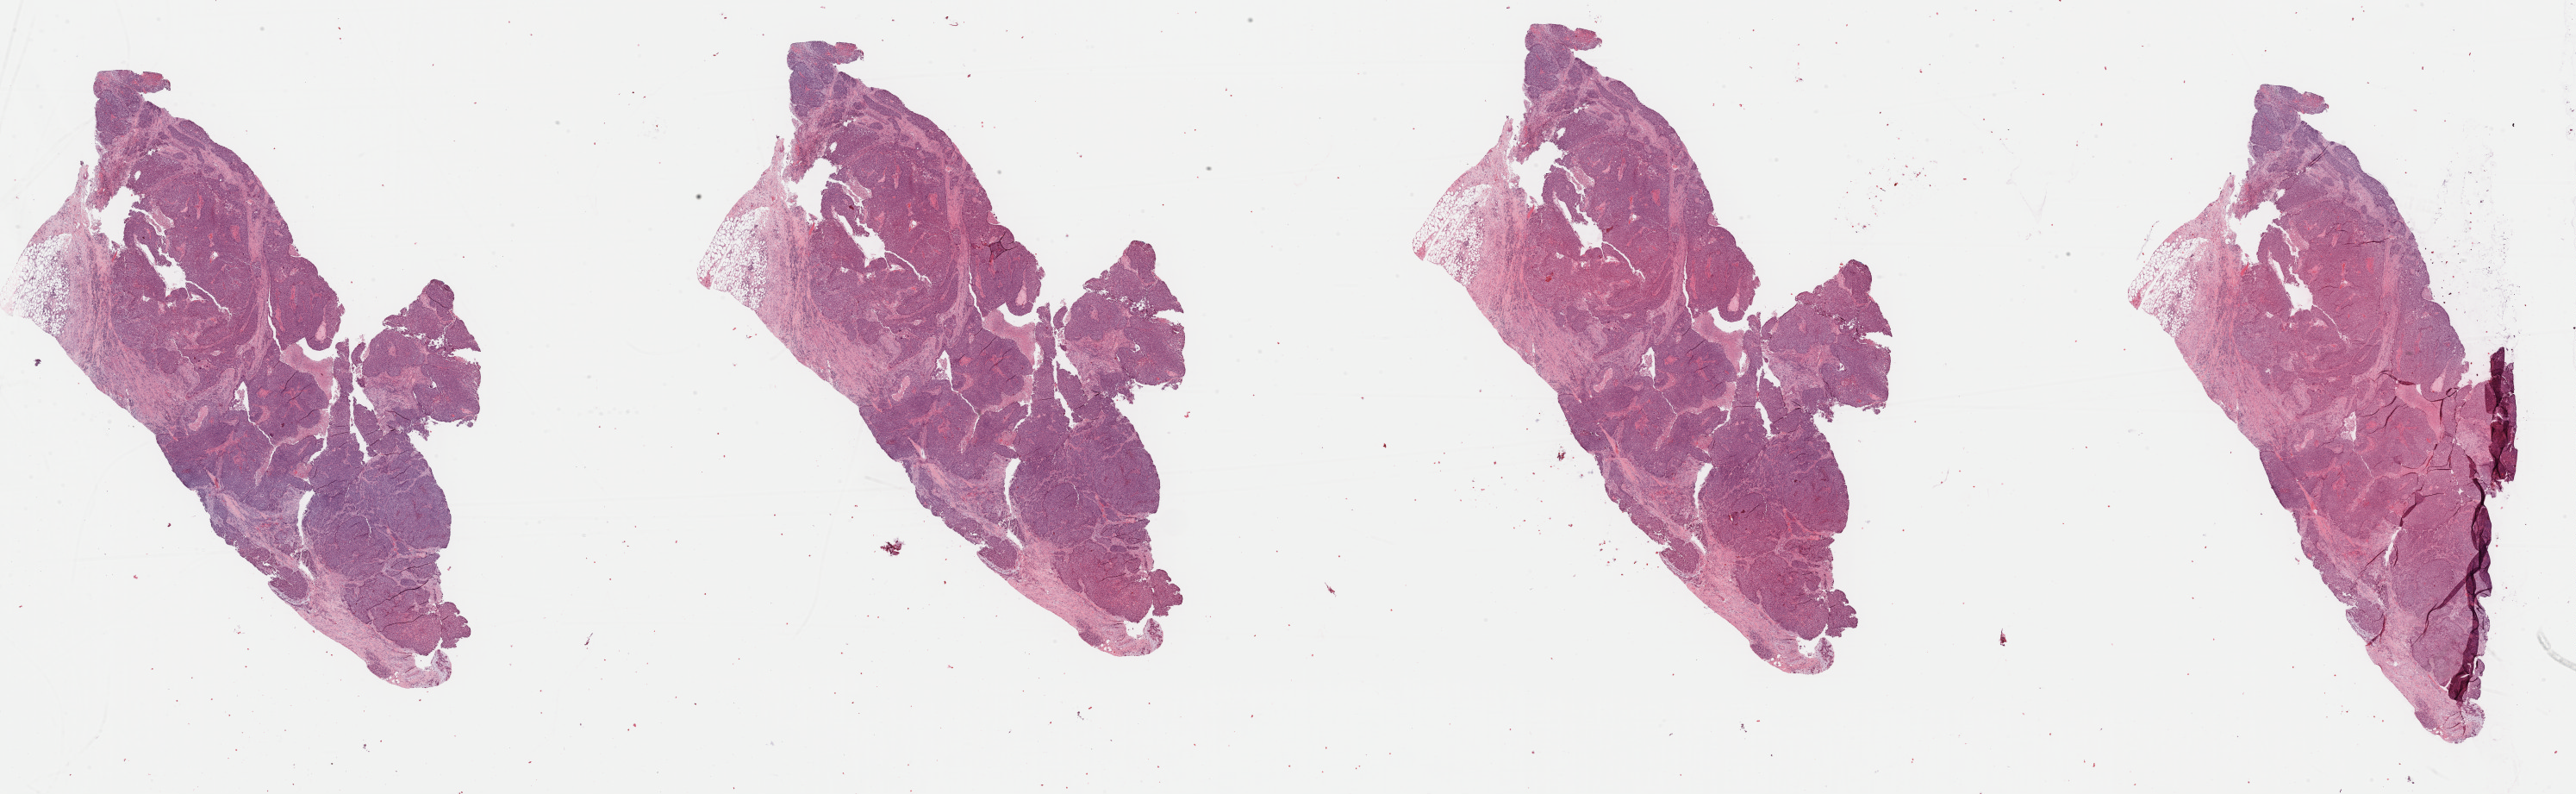
Whole-slide histology image, H&E-stained, low-resolution overview of the scanned area, about 47.2 x 14.5 mm (acquisition: 40x scan), FFPE section, primary tumour sample from the breast. Patient: female, age at initial diagnosis 57 years.
* AJCC pathologic stage: IIA
* diagnosis: Infiltrating duct carcinoma, NOS
* lymph nodes positive (case pathology): 0 of 1 examined